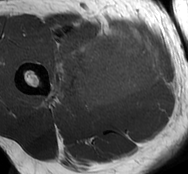
MRI of an extremity soft-tissue mass, one axial slice. Position 32 of 93 along the scan axis. MR volume resampled by the dataset authors to the PET/CT grid (not the native acquisition matrix). 3.27 mm slice thickness. 188 × 174 image matrix, field of view 184 × 170 mm. Male patient. Case-level facts recorded for this patient, not image findings: histological type: undifferentiated - pleiomorphic; grade: high; site of the primary tumour: right thigh.
Annotated regions visible in this slice (expert contour drawn on MRI and transferred to this co-registered scan by the dataset authors):
- gross tumour volume including surrounding oedema: bounding box (x1, y1, x2, y2) in pixels: (49, 24, 162, 107)
- gross tumour volume (mass): (74, 28, 160, 107)